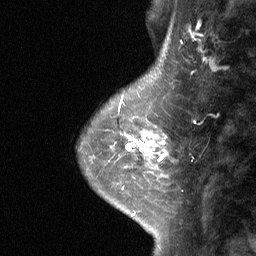
Breast MRI (dynamic contrast-enhanced), one sagittal slice. Slice 17 of 64 in the series (ordered by position). Dynamic contrast-enhanced study with each time point stored as its own series, time point 2 of 3 at this slice position (early post-contrast, ordered by acquisition time). 1.5 T. TE 4.8 ms, TR 27 ms. 2 mm slice thickness. 256 × 256 image matrix. Female patient, age 42 years. From the clinical record (not read from this slice): setting: breast cancer imaged before/during neoadjuvant chemotherapy; receptor status: triple-negative.
Structures marked on this image (semi-automatically segmented with operator editing):
- analysis volume of interest (the breast-tissue region the enhancement analysis was run in; not a lesion): bounding box (x1, y1, x2, y2) in pixels: (111, 104, 170, 178)
- tumour enhancement mask (voxels above the 90 % enhancement threshold inside the analysis volume of interest): (124, 130, 167, 161)